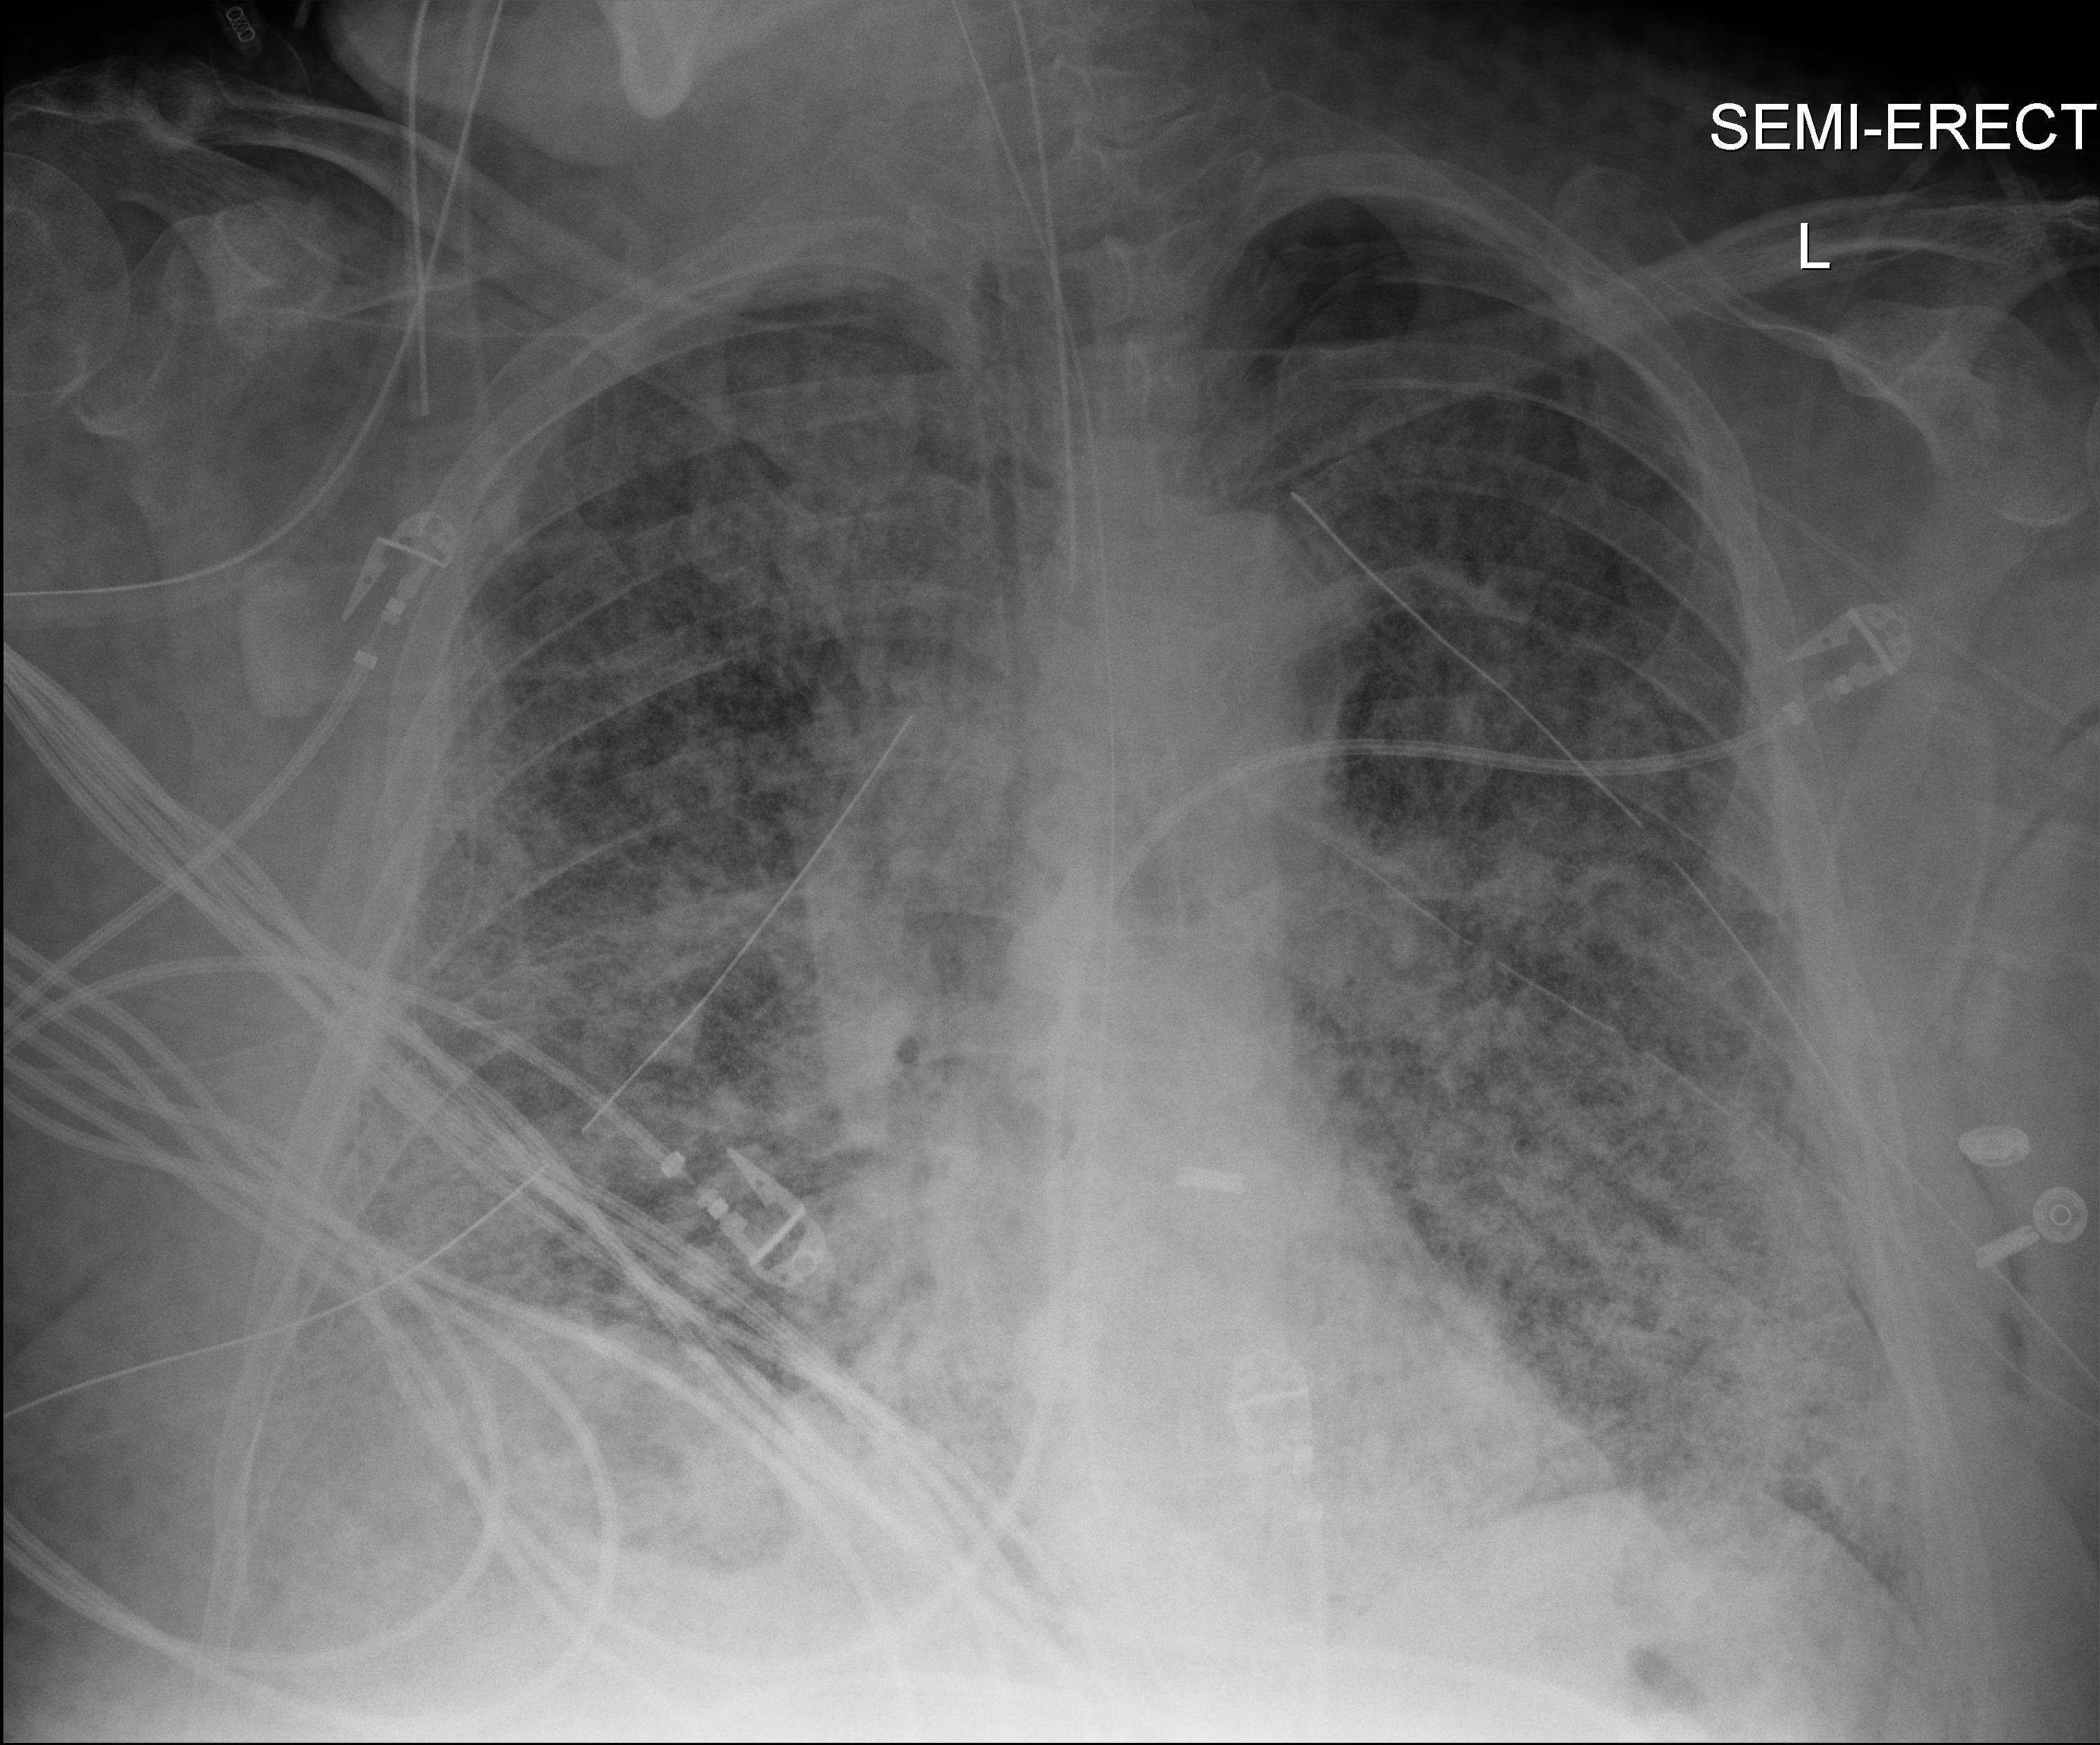
Portable chest radiograph. Adult patient hospitalised with COVID-19, age 18–59 years.
Admission-level facts for this patient (not findings on this image; timing relative to this image not recorded):
- smoking status (admission record): never
- length of hospital stay: 28 days
- mechanically ventilated during this hospital stay: yes